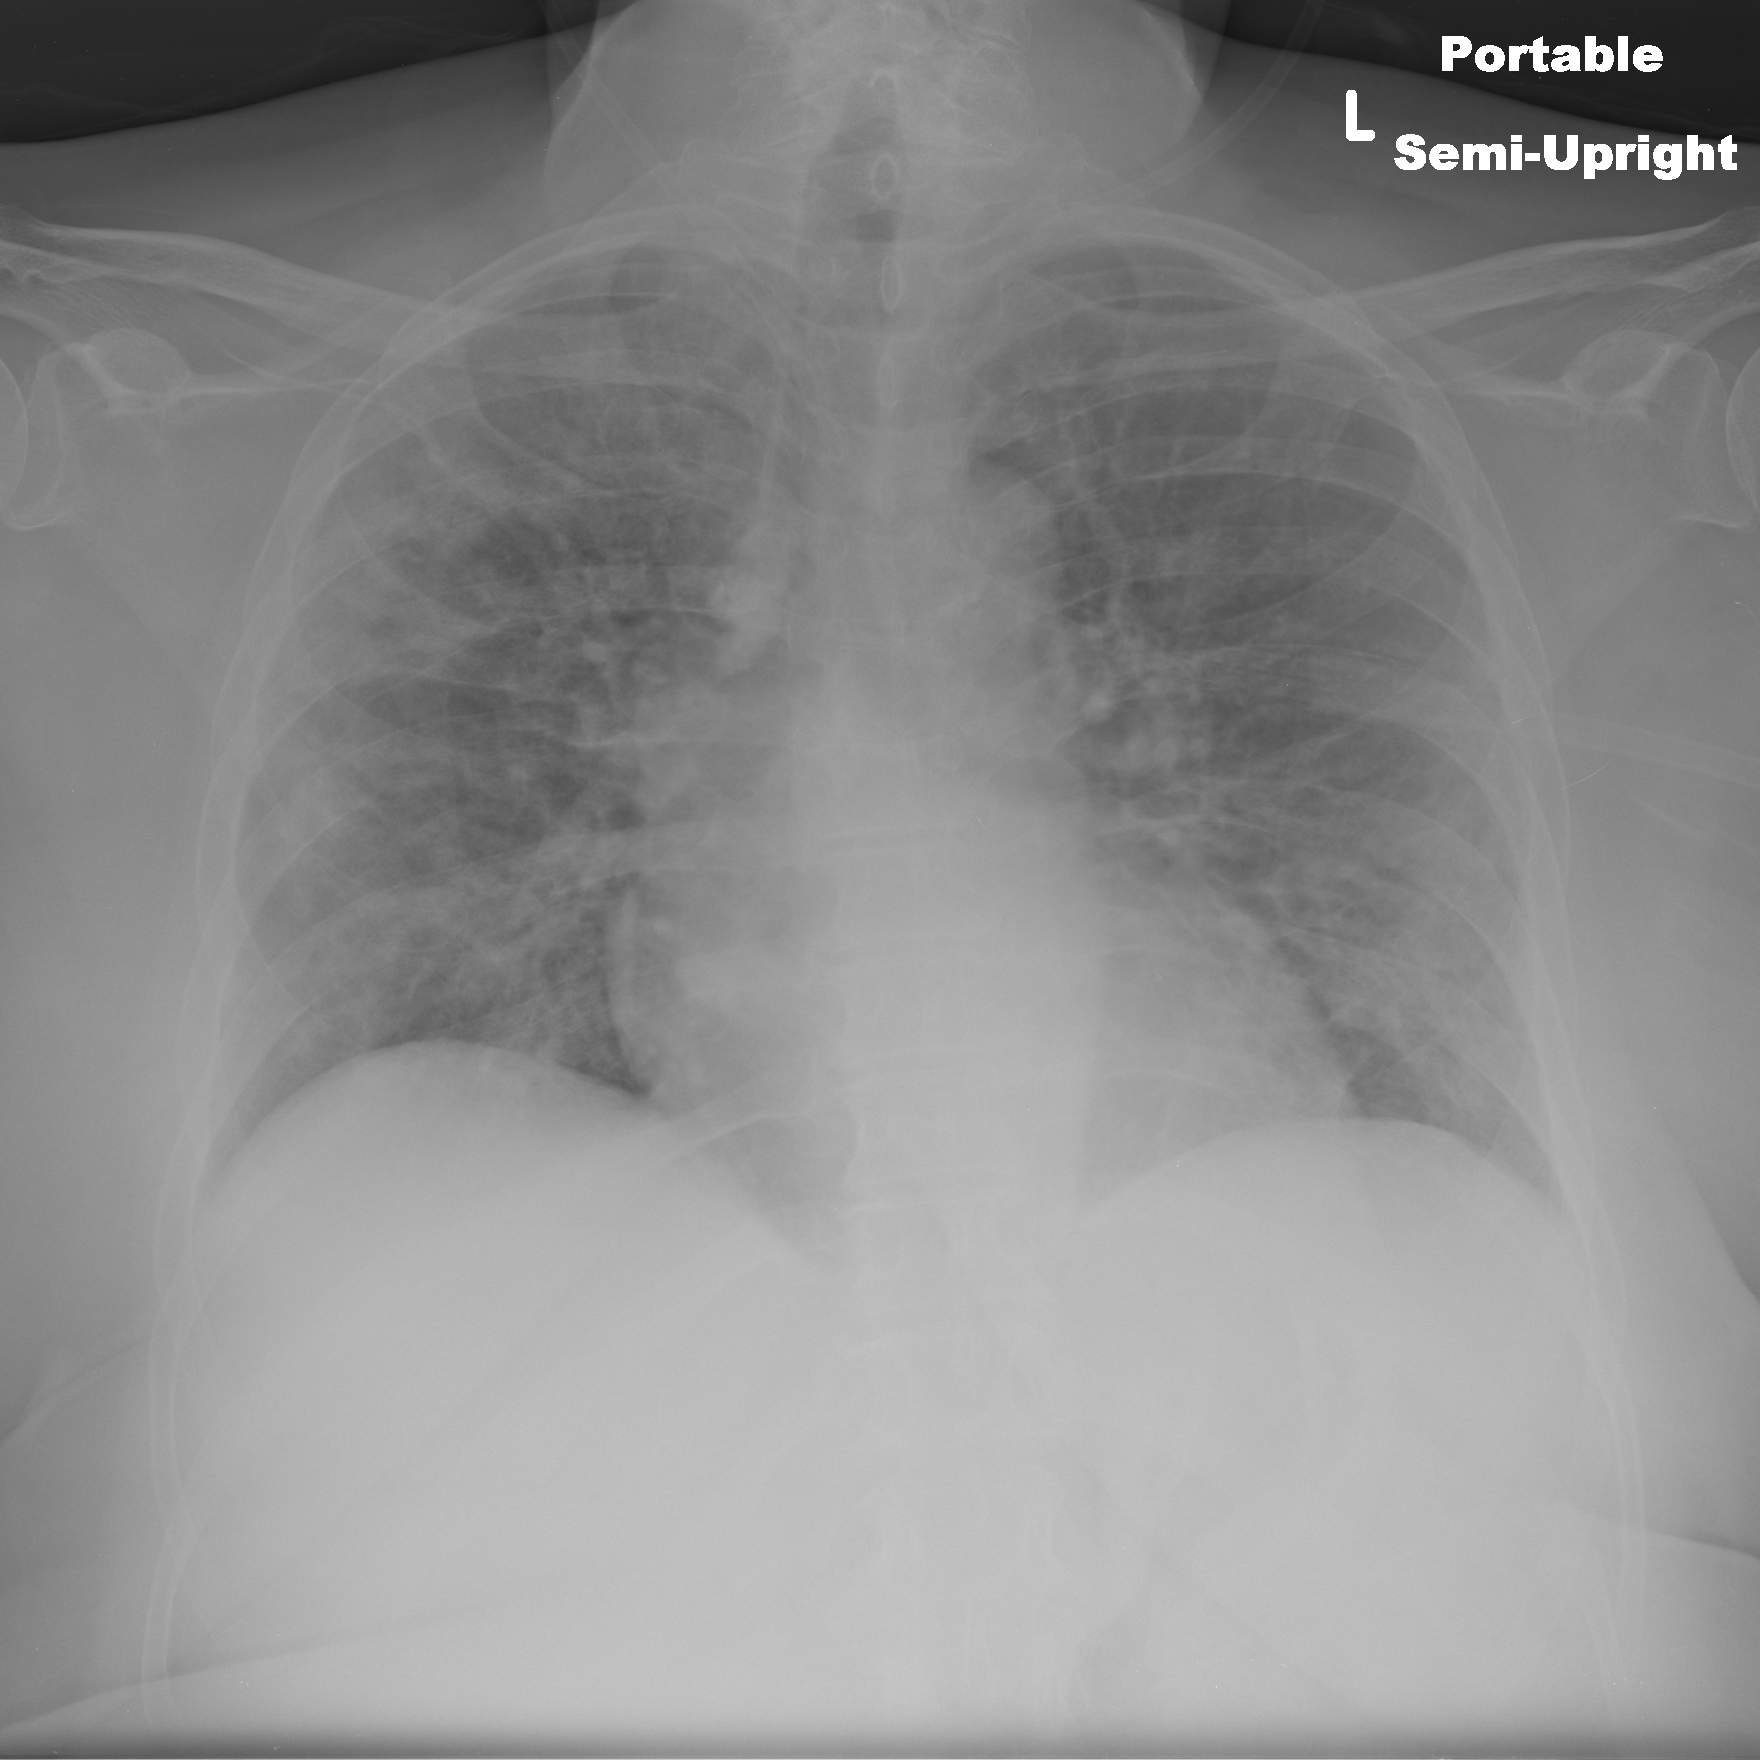
Chest X-ray (portable), AP projection. Female patient, age 59 years; imaged 7 days after the COVID-19 diagnosis.
Key findings recorded by the radiologist: patchy lung opacities noted bilaterally which are slightly increased from the prior examination.